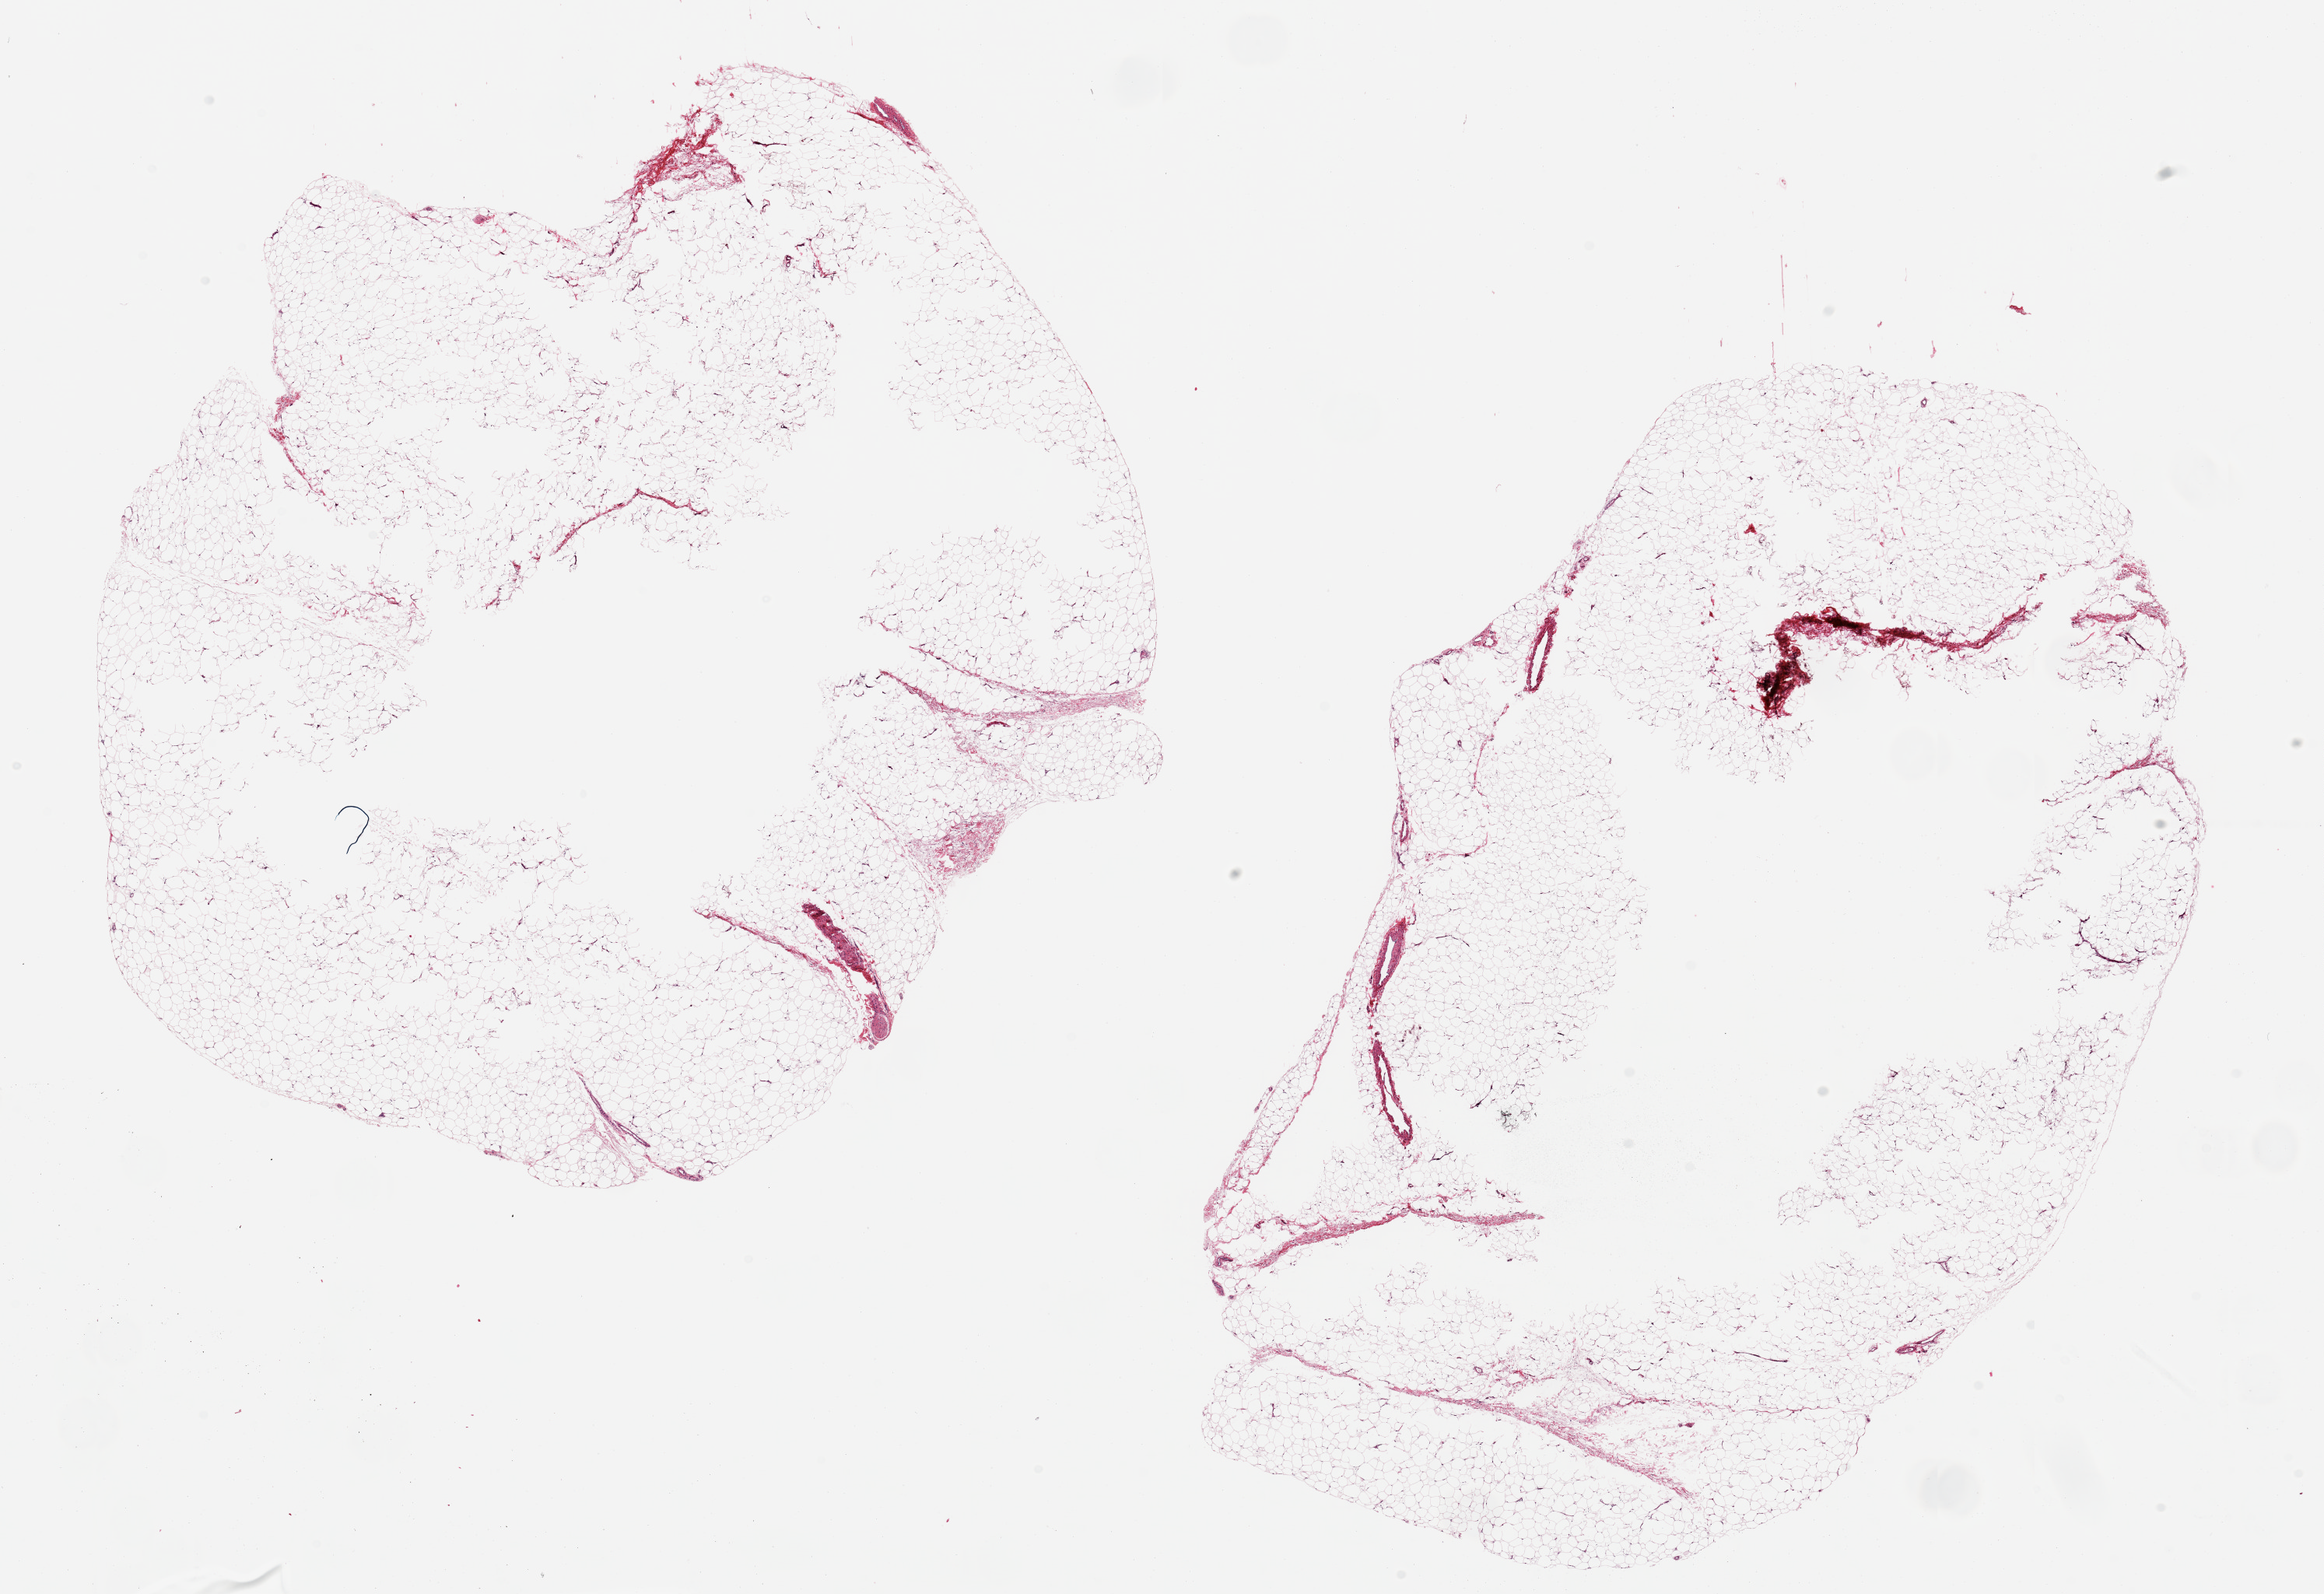
Hematoxylin and eosin (H&E) whole-slide image, a low-resolution overview of the entire scanned area, about 23.6 x 16.2 mm (from a 20x scan). PAXgene-fixed, paraffin-embedded tissue. Section of adipose tissue (target tissue). Tissue donor sample. Donor: female.
• pathologist's review note for this sample: 2 ~11x9mm aliquots. Large areas of central under-fixation with holes/tears